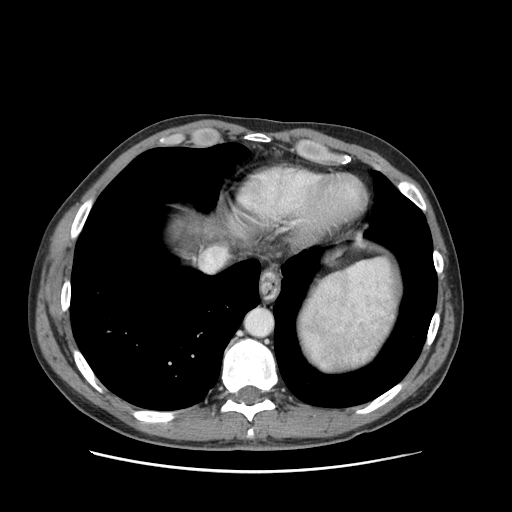
Contrast-enhanced abdominal CT (liver protocol), one axial slice. Slice 85 of 93 in the series (ordered by position). Reconstruction kernel STANDARD. 120 kVp. Soft-tissue window (W 400 / L 40 HU). 2.5 mm slice thickness. 512 × 512 image matrix, field of view 380 × 380 mm. From the clinical record (not read from this slice): diagnosis: hepatocellular carcinoma (patient treated with transarterial chemoembolisation; whether this scan precedes or follows treatment is not stated here); TNM stage (as recorded): Stage-II.
Annotated regions visible in this slice (semi-automatic segmentation, software-assisted and operator-edited):
- liver parenchyma outside the tumour (the mass and vessels are separate outlines, so this box may not span the whole liver): bounding box (x1, y1, x2, y2) in pixels: (170, 216, 224, 248)